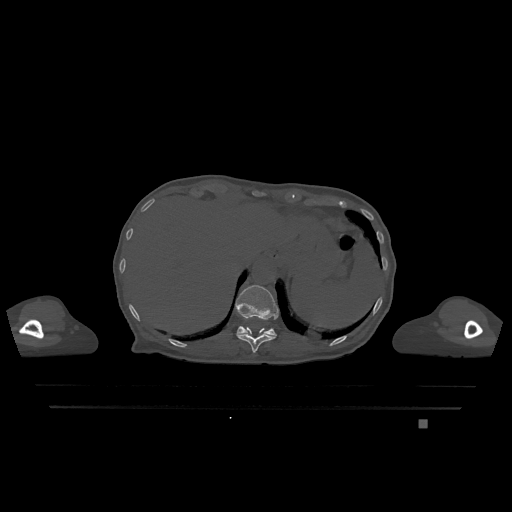
CT including the spine, one axial slice; position 565 of 1317 along the scan axis; bone window (W 1800 / L 400 HU); 512 × 512 image matrix. Female patient, age 74 years. Case-level facts recorded for this patient, not image findings: primary cancer: lung; vertebrae with lytic lesions (as recorded): T1, T4, T5, T6, L4, L5.
Annotated regions visible in this slice (semi-automatically segmented with operator editing):
- T11 vertebra: box from (x=236, y=327) to (x=276, y=353) px
- T12 vertebra: (x=236, y=285)–(x=279, y=336)